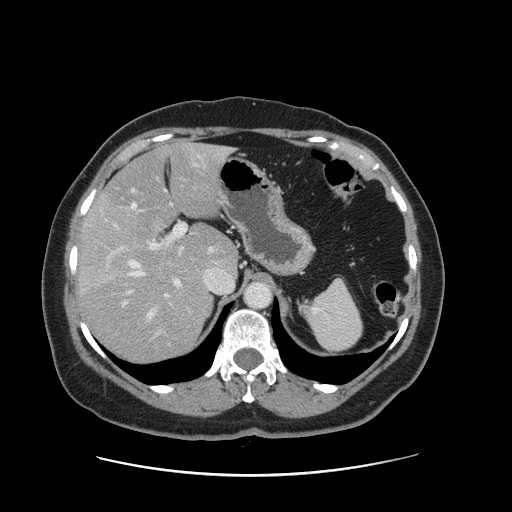
Contrast-enhanced abdominal CT, one axial slice; slice 102 of 161 in the series (ordered by position); soft-tissue window (W 400 / L 40 HU); 2.5 mm slice thickness; 512 × 512 image matrix, field of view 398 × 398 mm. Female patient, age 62 years. Case-level facts recorded for this patient, not image findings: diagnosis: colorectal cancer liver metastases, imaged before liver resection; multiple liver metastases: no; largest metastasis: 2.5 cm.
Outlined on this slice (expert manual segmentation):
- hepatic veins: bounding box [x1, y1, x2, y2] px = [129, 150, 233, 319]
- liver: [80, 144, 237, 362]
- planned liver remnant (the part of the liver to remain after resection): [102, 143, 237, 272]
- portal vein (with intrahepatic branches): [121, 190, 187, 338]